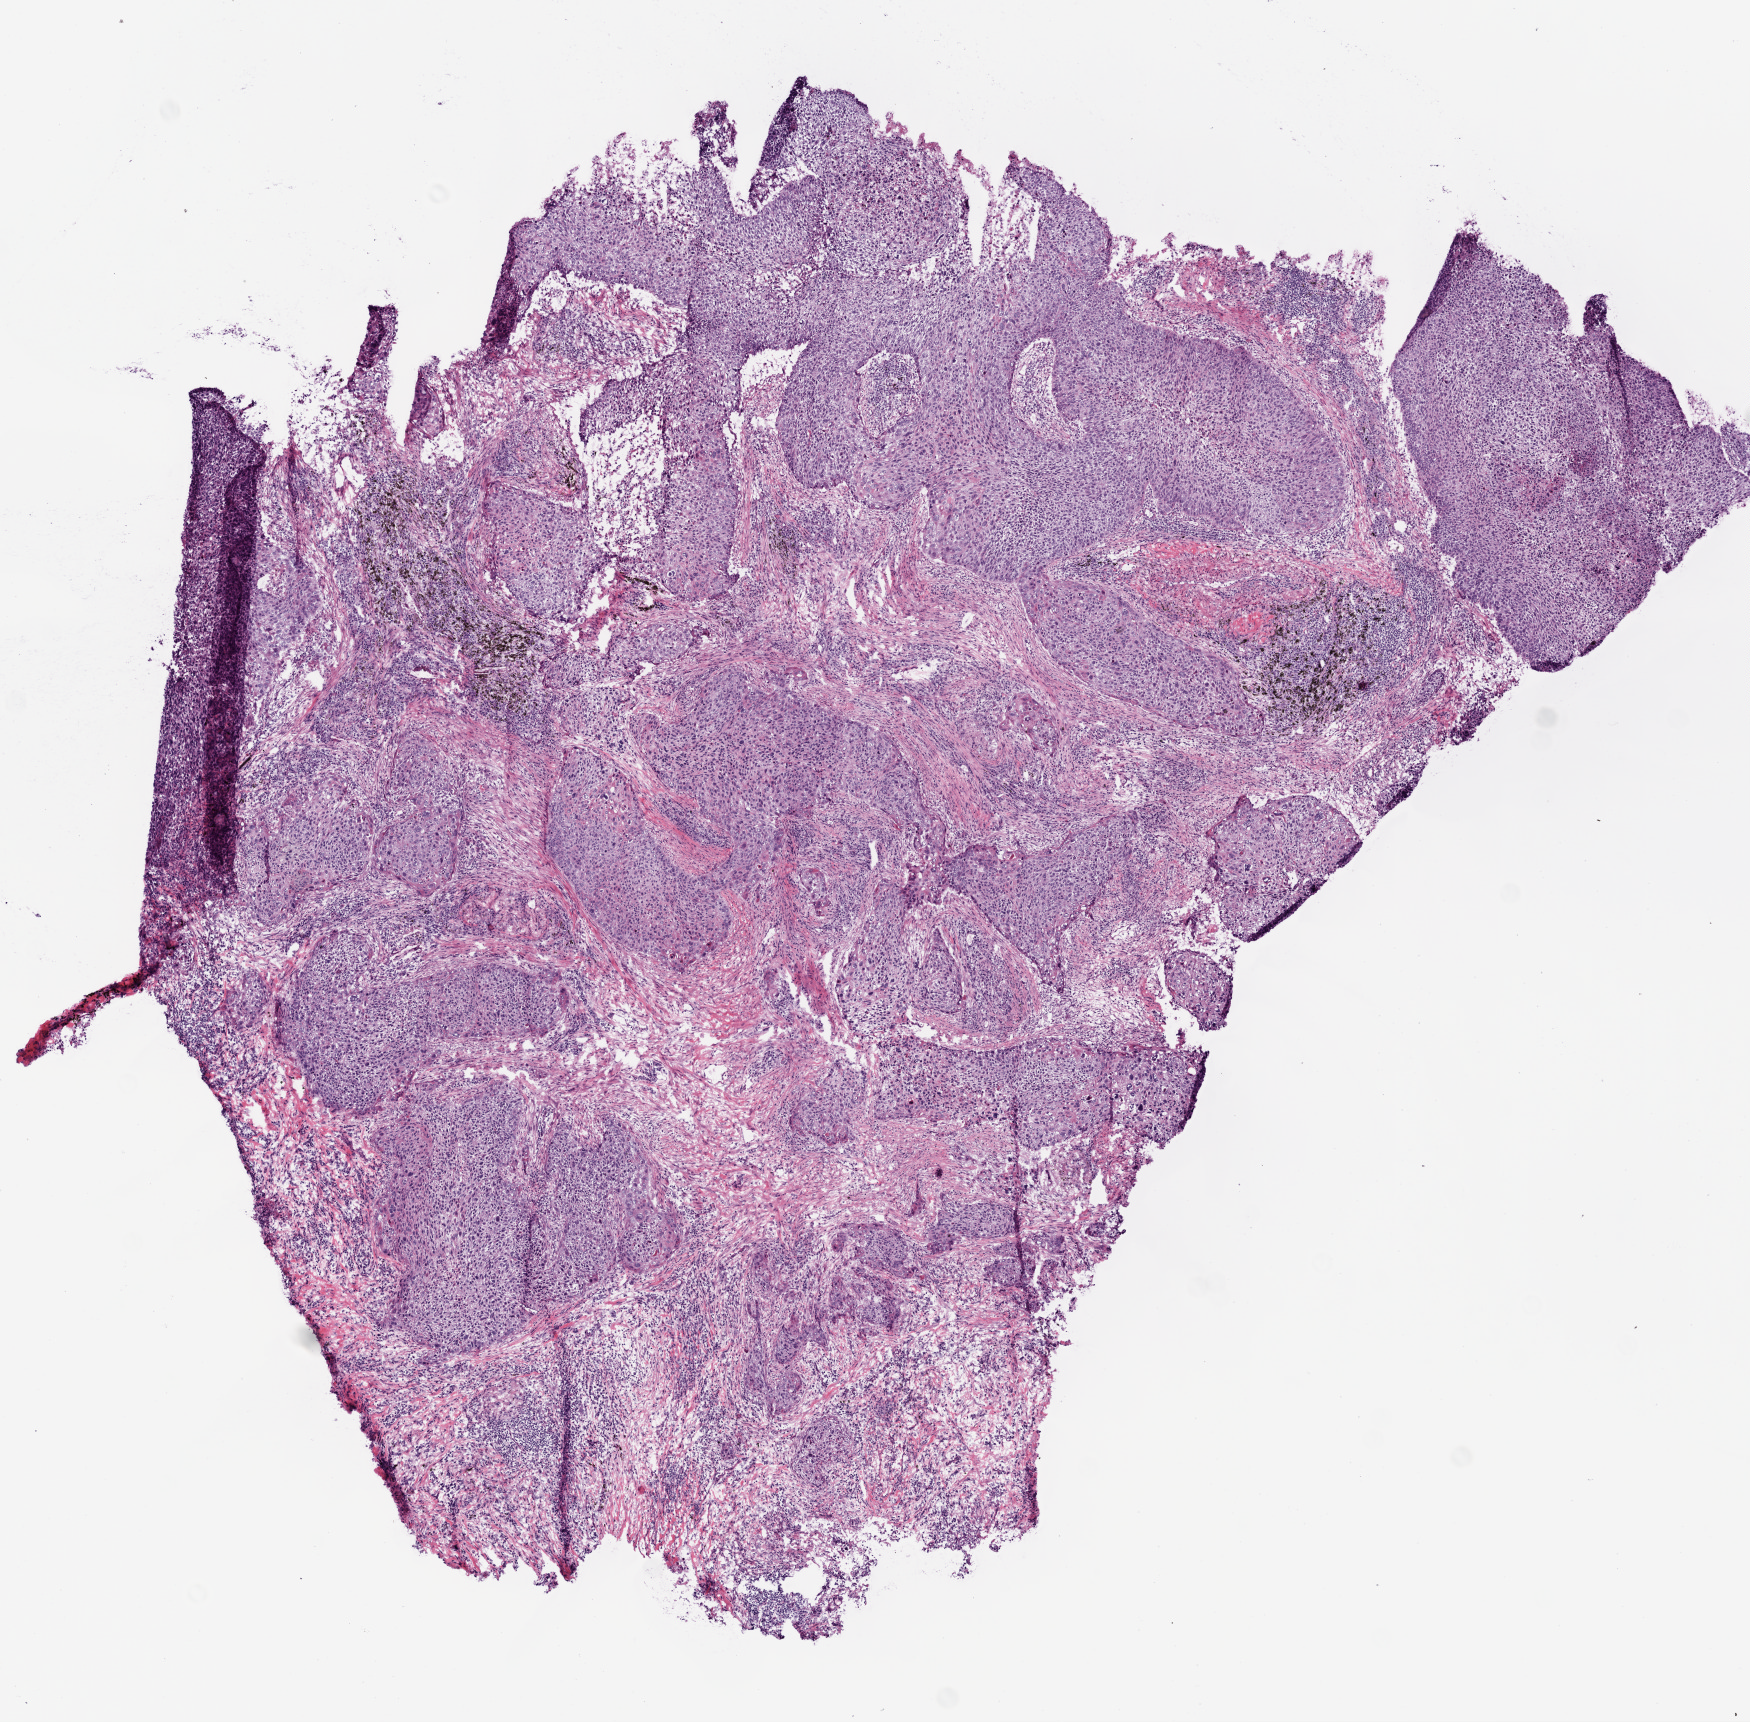
Whole-slide histology image, H&E-stained — whole scanned area (about 7.0 x 6.9 mm) shown as a low-resolution overview; frozen section from the top of the tissue portion; sample: primary tumour, lung. Patient: male, age at initial diagnosis 70 years. Composition of this section per pathologist review: tumour cells 60%, tumour nuclei 80%, normal cells 0%, stromal cells 35%, necrosis 5%. Infiltration values recorded for this section: lymphocyte infiltration 5%.
AJCC pathologic stage: IV. Histologic diagnosis: Squamous cell carcinoma, NOS (upper lobe, lung).